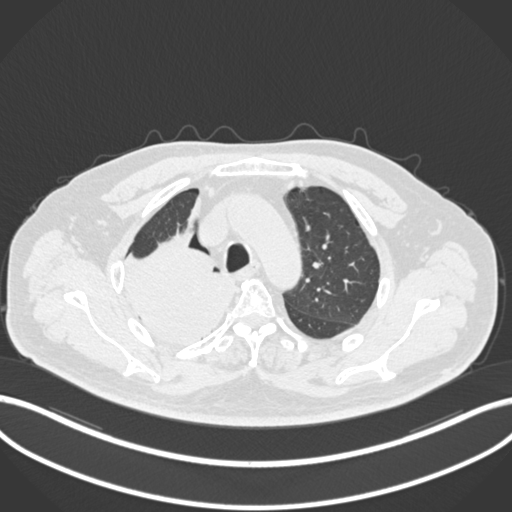
Chest CT, one axial slice; reconstruction kernel B30f; 120 kVp; lung window (W 1500 / L -600 HU); 1 mm slice thickness; 512 × 512 image matrix. Patient: male, 68 years. Case-level facts recorded for this patient, not image findings: clinical TNM (as recorded): T2a N0 M0.
Annotated regions visible in this slice (rectangle marked by the reading radiologist):
- lung tumour (recorded histology: adenocarcinoma): box from (x=114, y=217) to (x=241, y=351) px